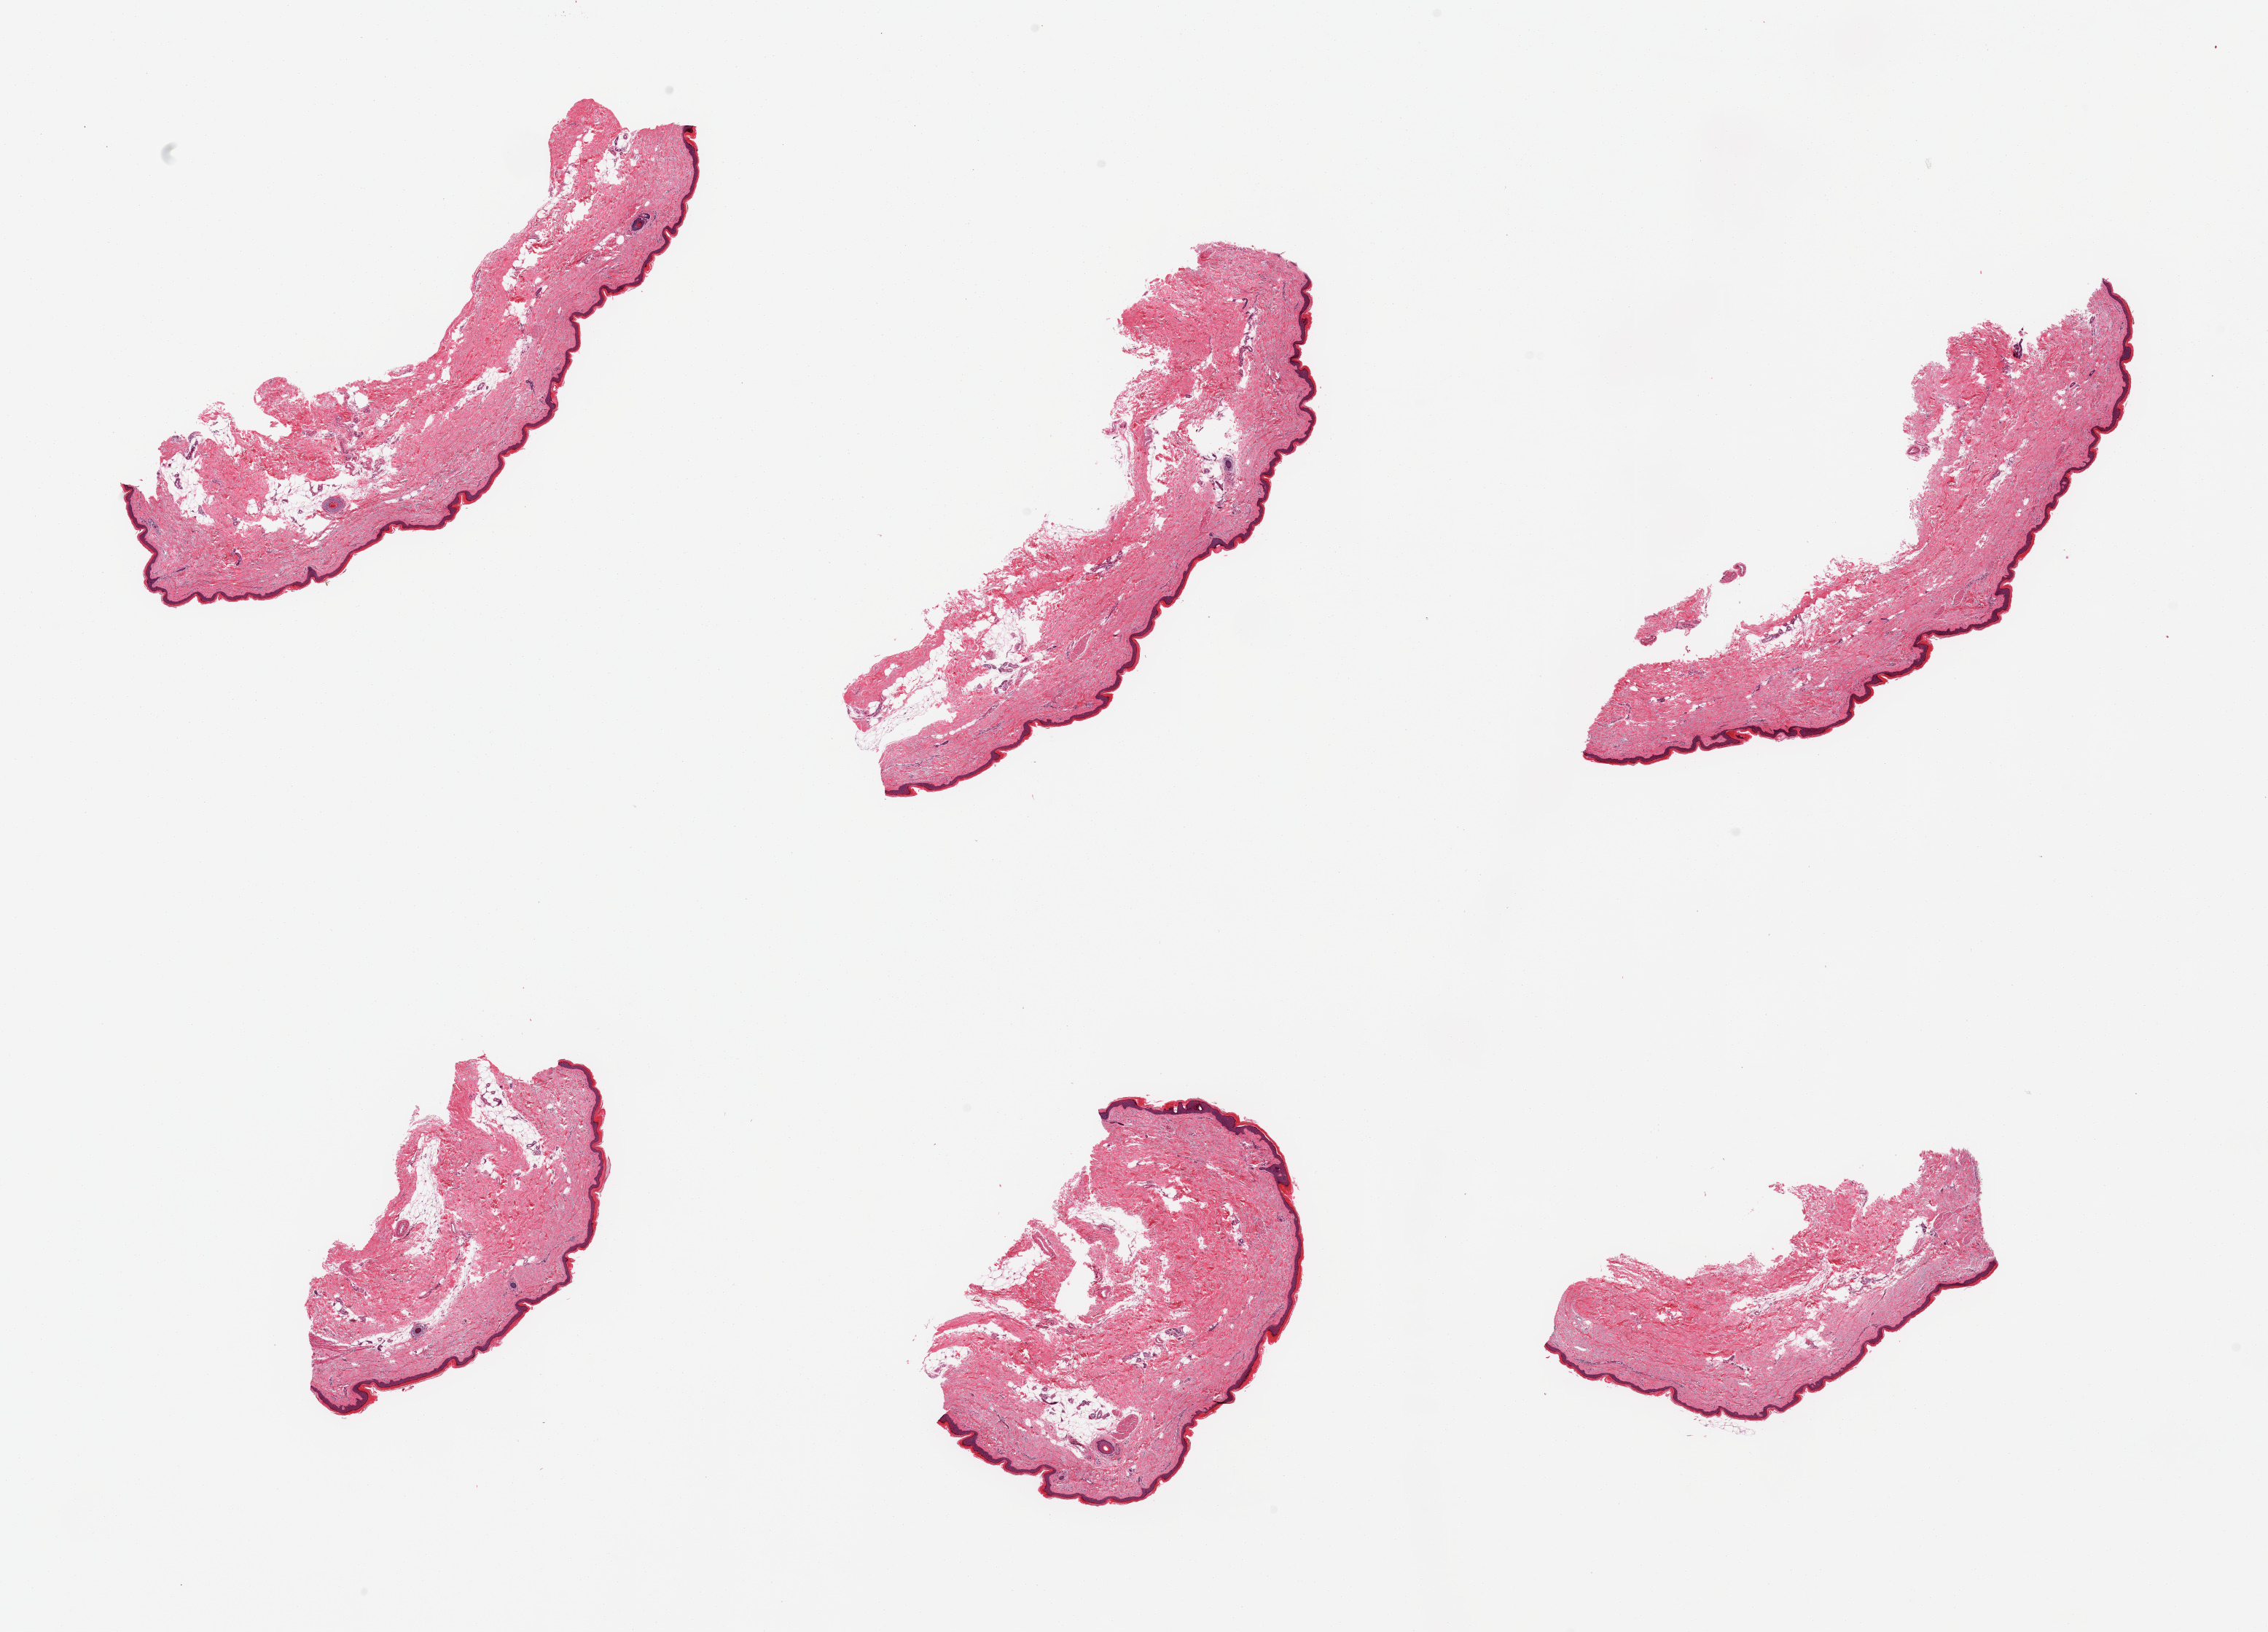
Hematoxylin and eosin (H&E) whole-slide image — a low-resolution overview of the entire scanned area, about 24.6 x 17.7 mm. PAXgene-fixed, paraffin-embedded tissue. Sampled site (target tissue): skin of lower leg. Tissue donor sample.
- review note (as recorded): 6 pieces; upp to 20% dermal fat; well trimmed